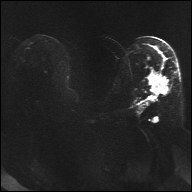
Breast MRI, one axial slice; position 18 of 32 along the scan axis; diffusion-weighted series; image 2 of 4 stored at this slice position (different b-values; order by instance number); 1.5 T; 4 mm slice thickness; 192 × 192 image matrix. Female patient.
Annotated regions visible in this slice (expert manual segmentation):
- tumour on diffusion-weighted imaging: bounding box [x1, y1, x2, y2] px = [149, 76, 169, 94]